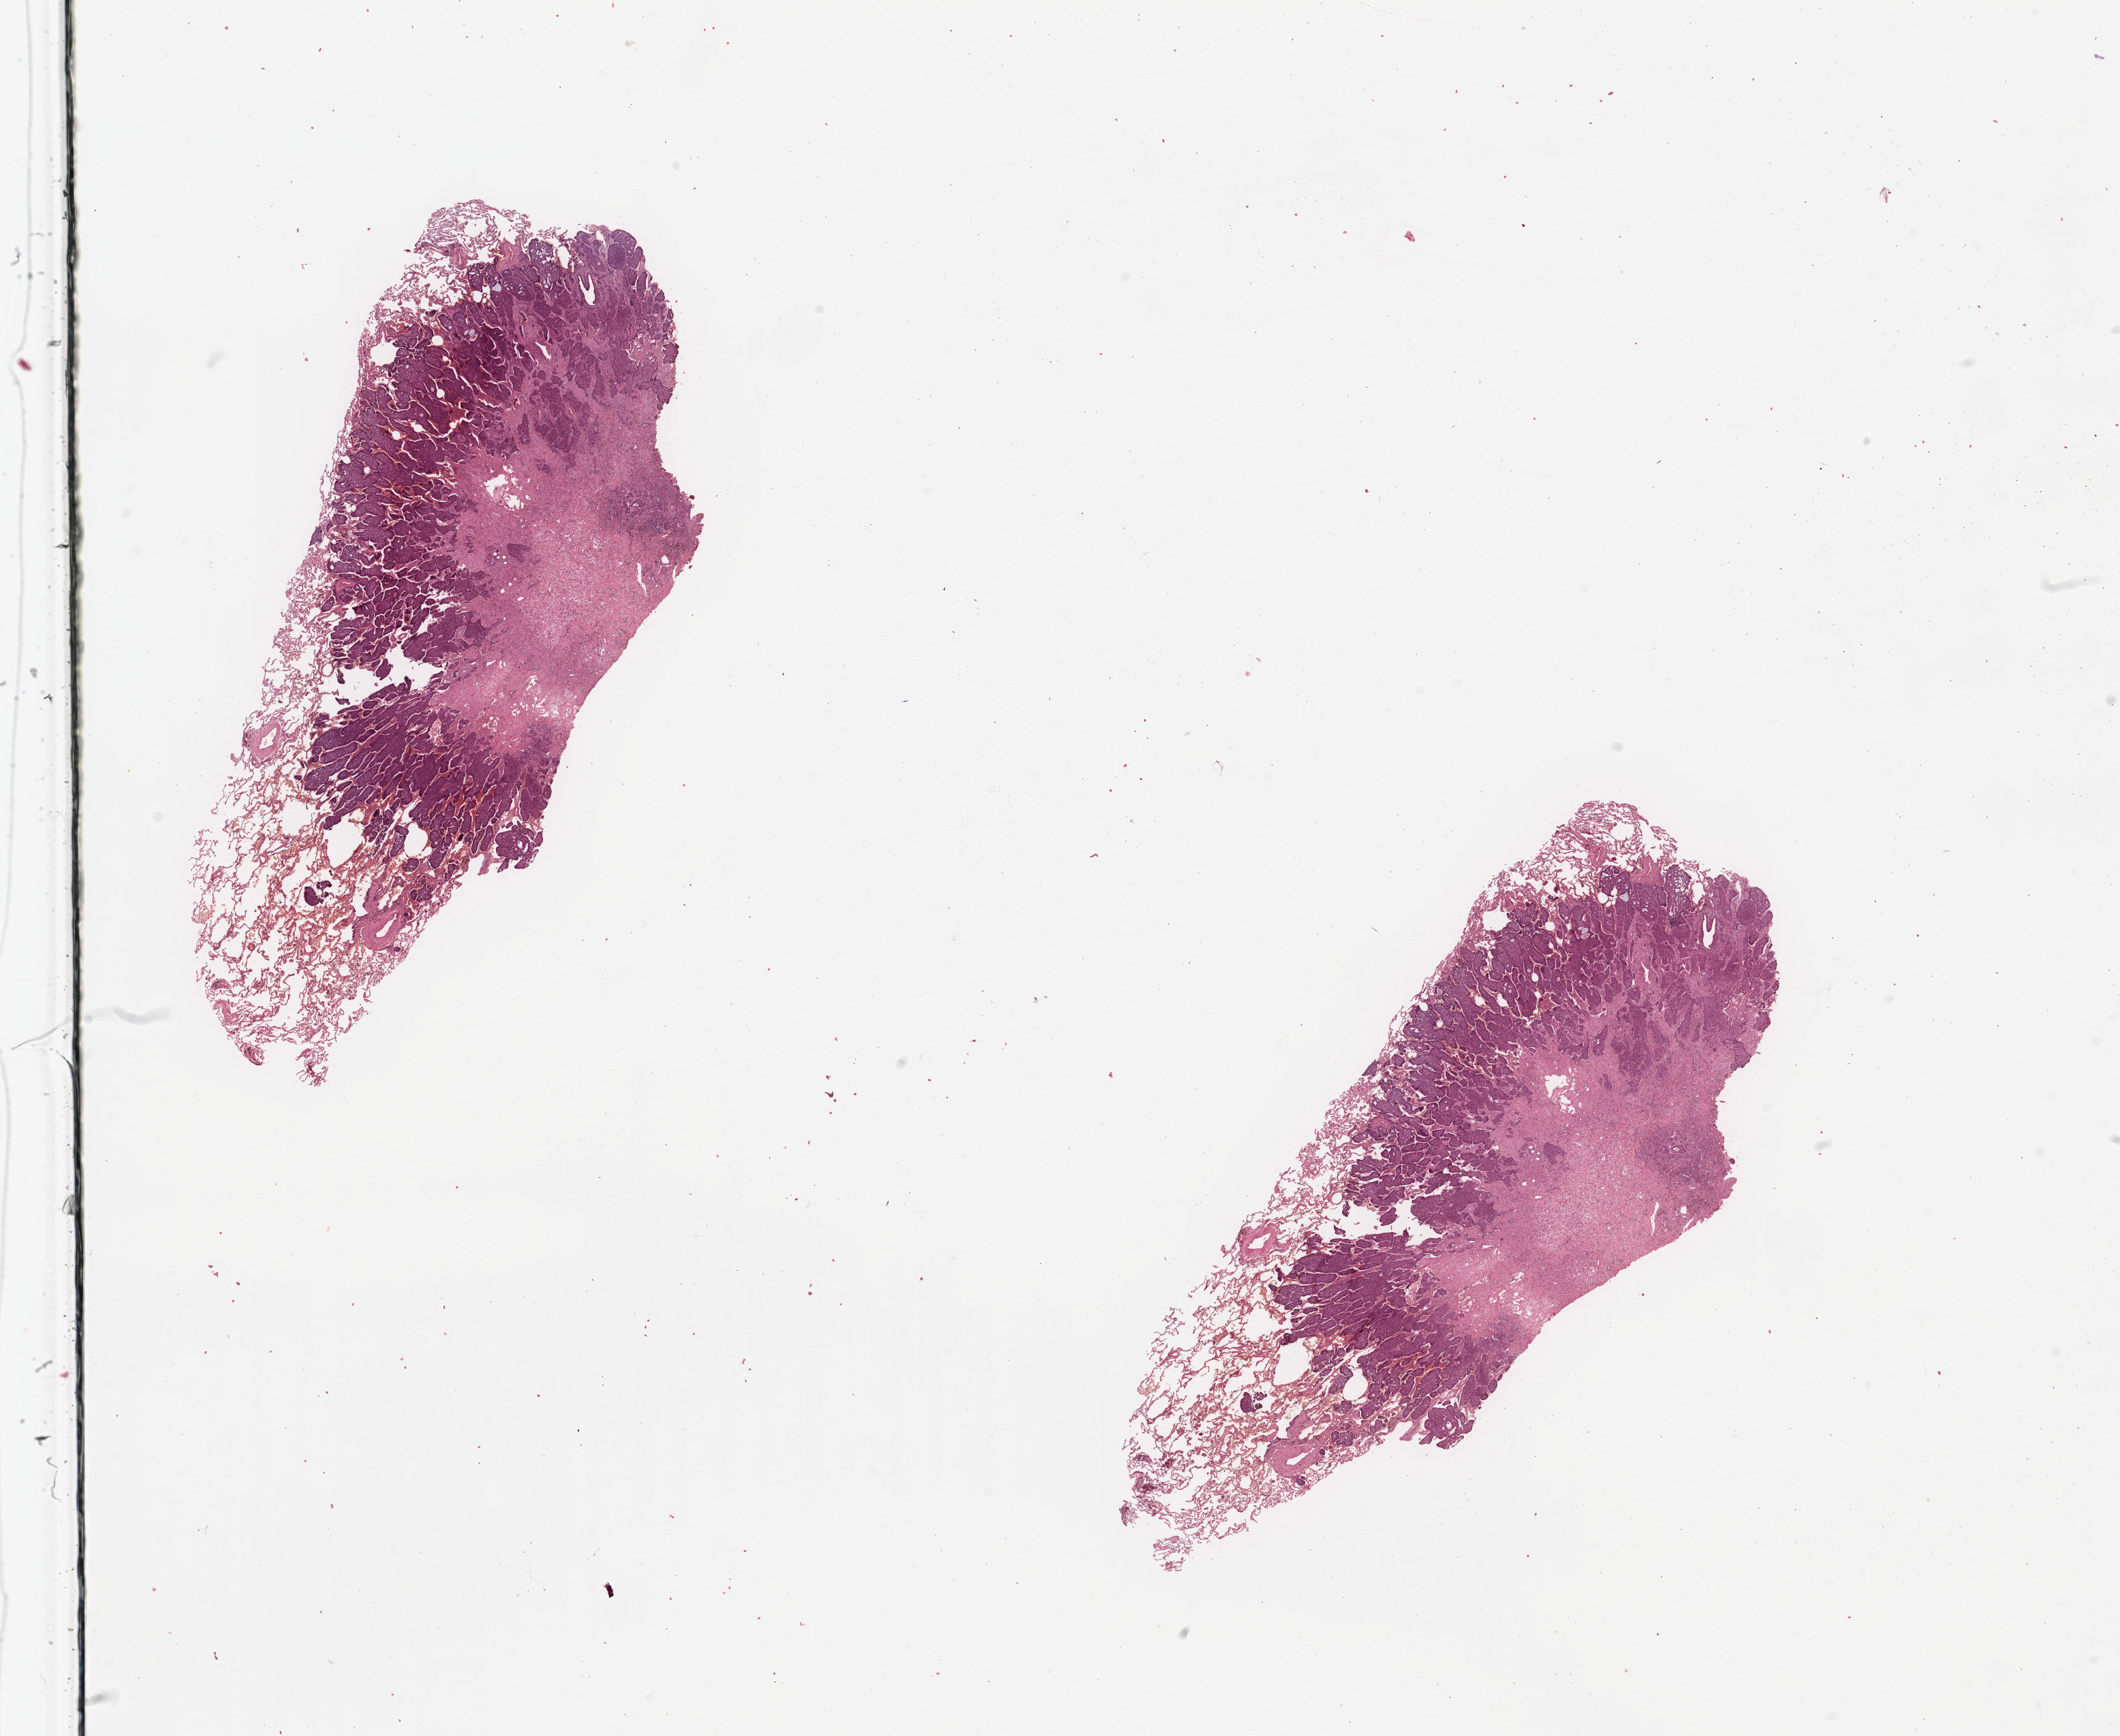
Digitized H&E tissue section (whole slide), low-resolution overview of the scanned area, about 24.6 x 20.2 mm; lung, tumour tissue. Patient: male, age 66 years.
Patient diagnosis (cohort enrolment): squamous cell carcinoma (lung).